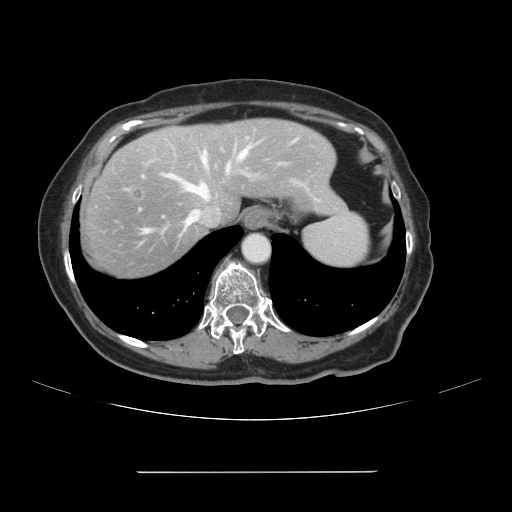
Contrast-enhanced abdominal CT, one axial slice; position 87 of 111 along the scan axis; intravenous contrast given; soft-tissue window (W 400 / L 40 HU); 2.5 mm slice thickness; 512 × 512 image matrix, field of view 400 × 400 mm. Female patient, age 74 years. Case-level facts recorded for this patient, not image findings: diagnosis: colorectal cancer liver metastases, imaged before liver resection; multiple liver metastases: yes; largest metastasis: 1.1 cm; disease in both lobes: yes.
Outlined on this slice (manually delineated by an expert):
- hepatic veins: bounding box <145,138,299,232> (left, top, right, bottom; pixels)
- liver: <79,119,344,280>
- planned liver remnant (the part of the liver to remain after resection): <168,119,344,218>
- portal vein (with intrahepatic branches): <229,164,231,167>
- liver metastasis: <130,188,145,200>